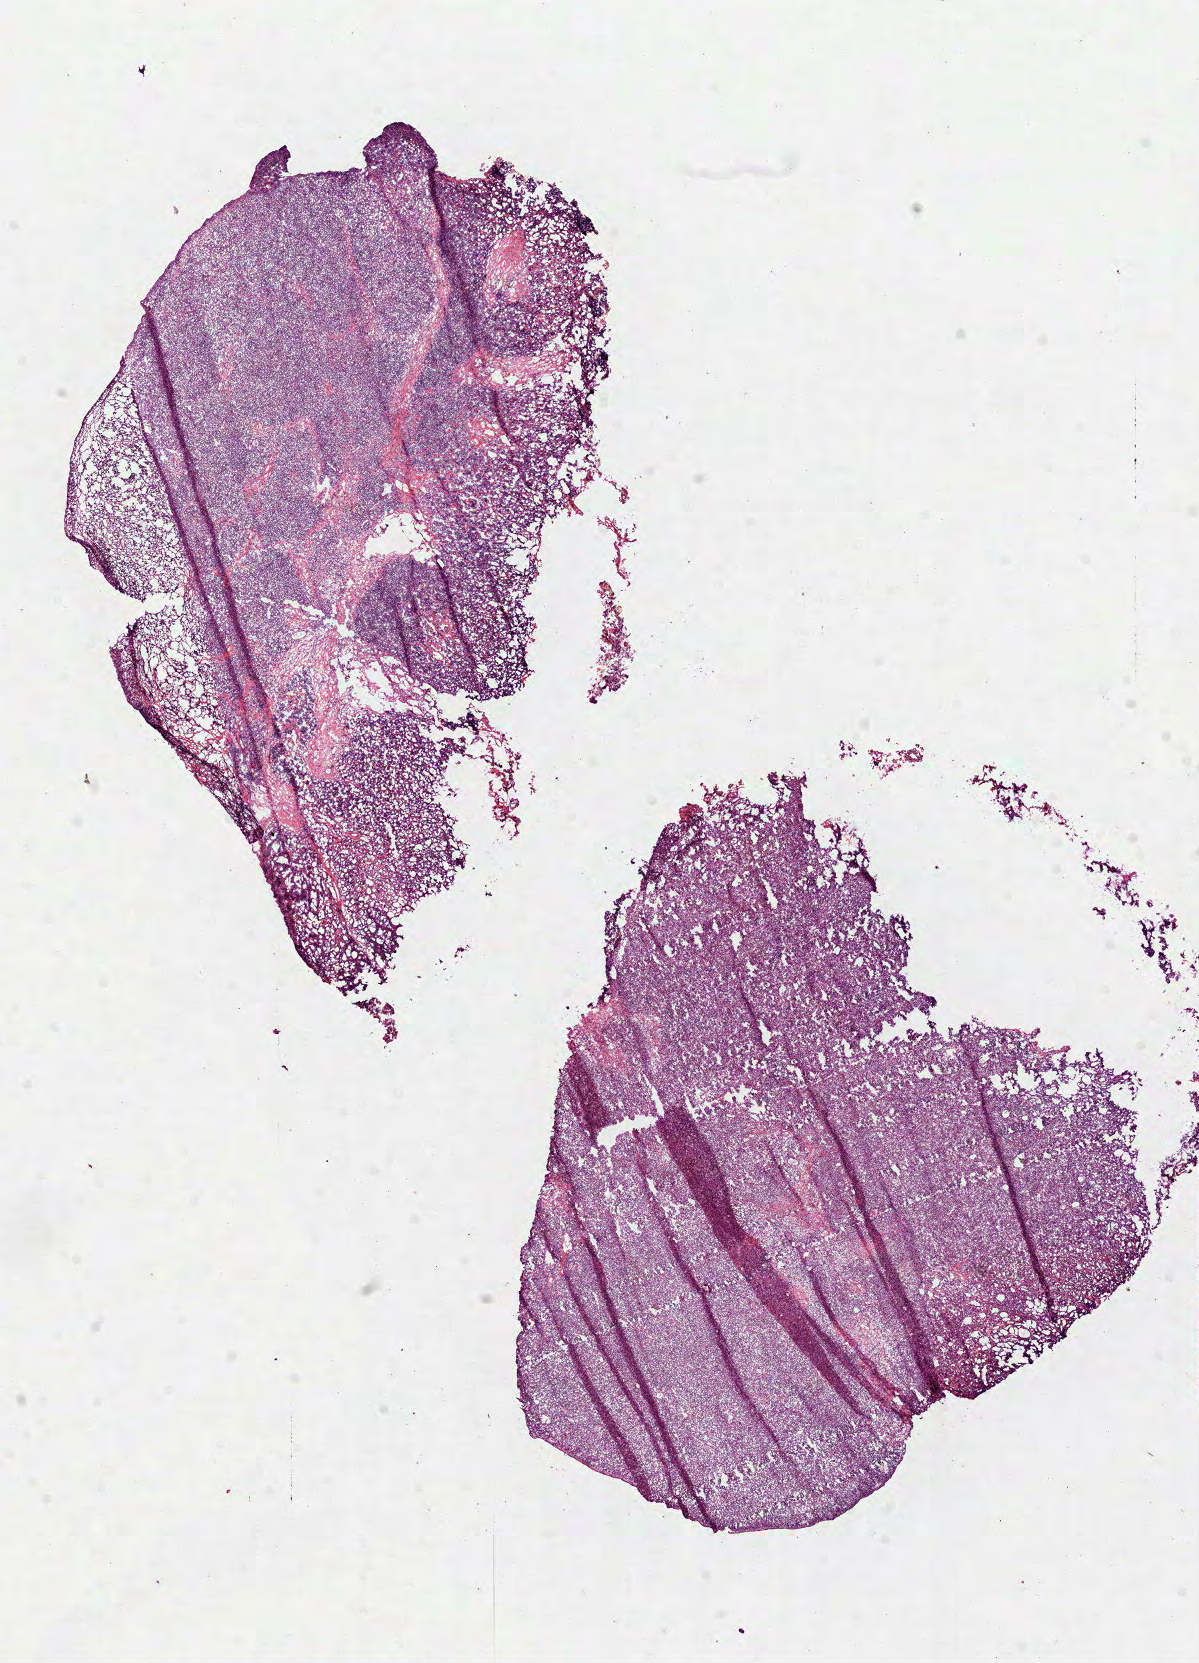
H&E whole-slide image — a low-resolution overview of the entire scanned area, about 9.7 x 13.4 mm (from a 40x scan). Frozen section from the bottom of the tissue portion. Lymphoid tissue, primary tumour sample. Male, age 52 years at initial diagnosis. Composition of this section per pathologist review: tumour cells 90%, tumour nuclei 85%, normal cells 0%, stromal cells 10%, necrosis 0%.
Pathologic diagnosis: Diffuse large B-cell lymphoma, NOS.